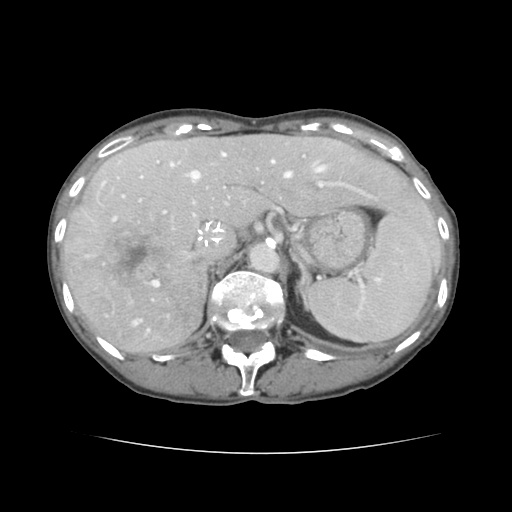
Contrast-enhanced abdominal CT, one axial slice; slice 99 of 136 in the series (ordered by position); 120 kVp; intravenous contrast given; soft-tissue window (W 400 / L 40 HU); 2.5 mm slice thickness; 512 × 512 image matrix, field of view 319 × 319 mm. Female patient, age 77 years. From the clinical record (not read from this slice): diagnosis: colorectal cancer liver metastases, imaged before liver resection; multiple liver metastases: yes; largest metastasis: 3 cm; disease in both lobes: no.
Outlined on this slice (manually delineated by an expert):
- hepatic veins: bounding box <133,153,325,331> (left, top, right, bottom; pixels)
- liver: <65,135,441,354>
- planned liver remnant (the part of the liver to remain after resection): <157,135,440,255>
- portal vein (with intrahepatic branches): <112,163,377,287>
- liver metastasis: <96,221,176,296>